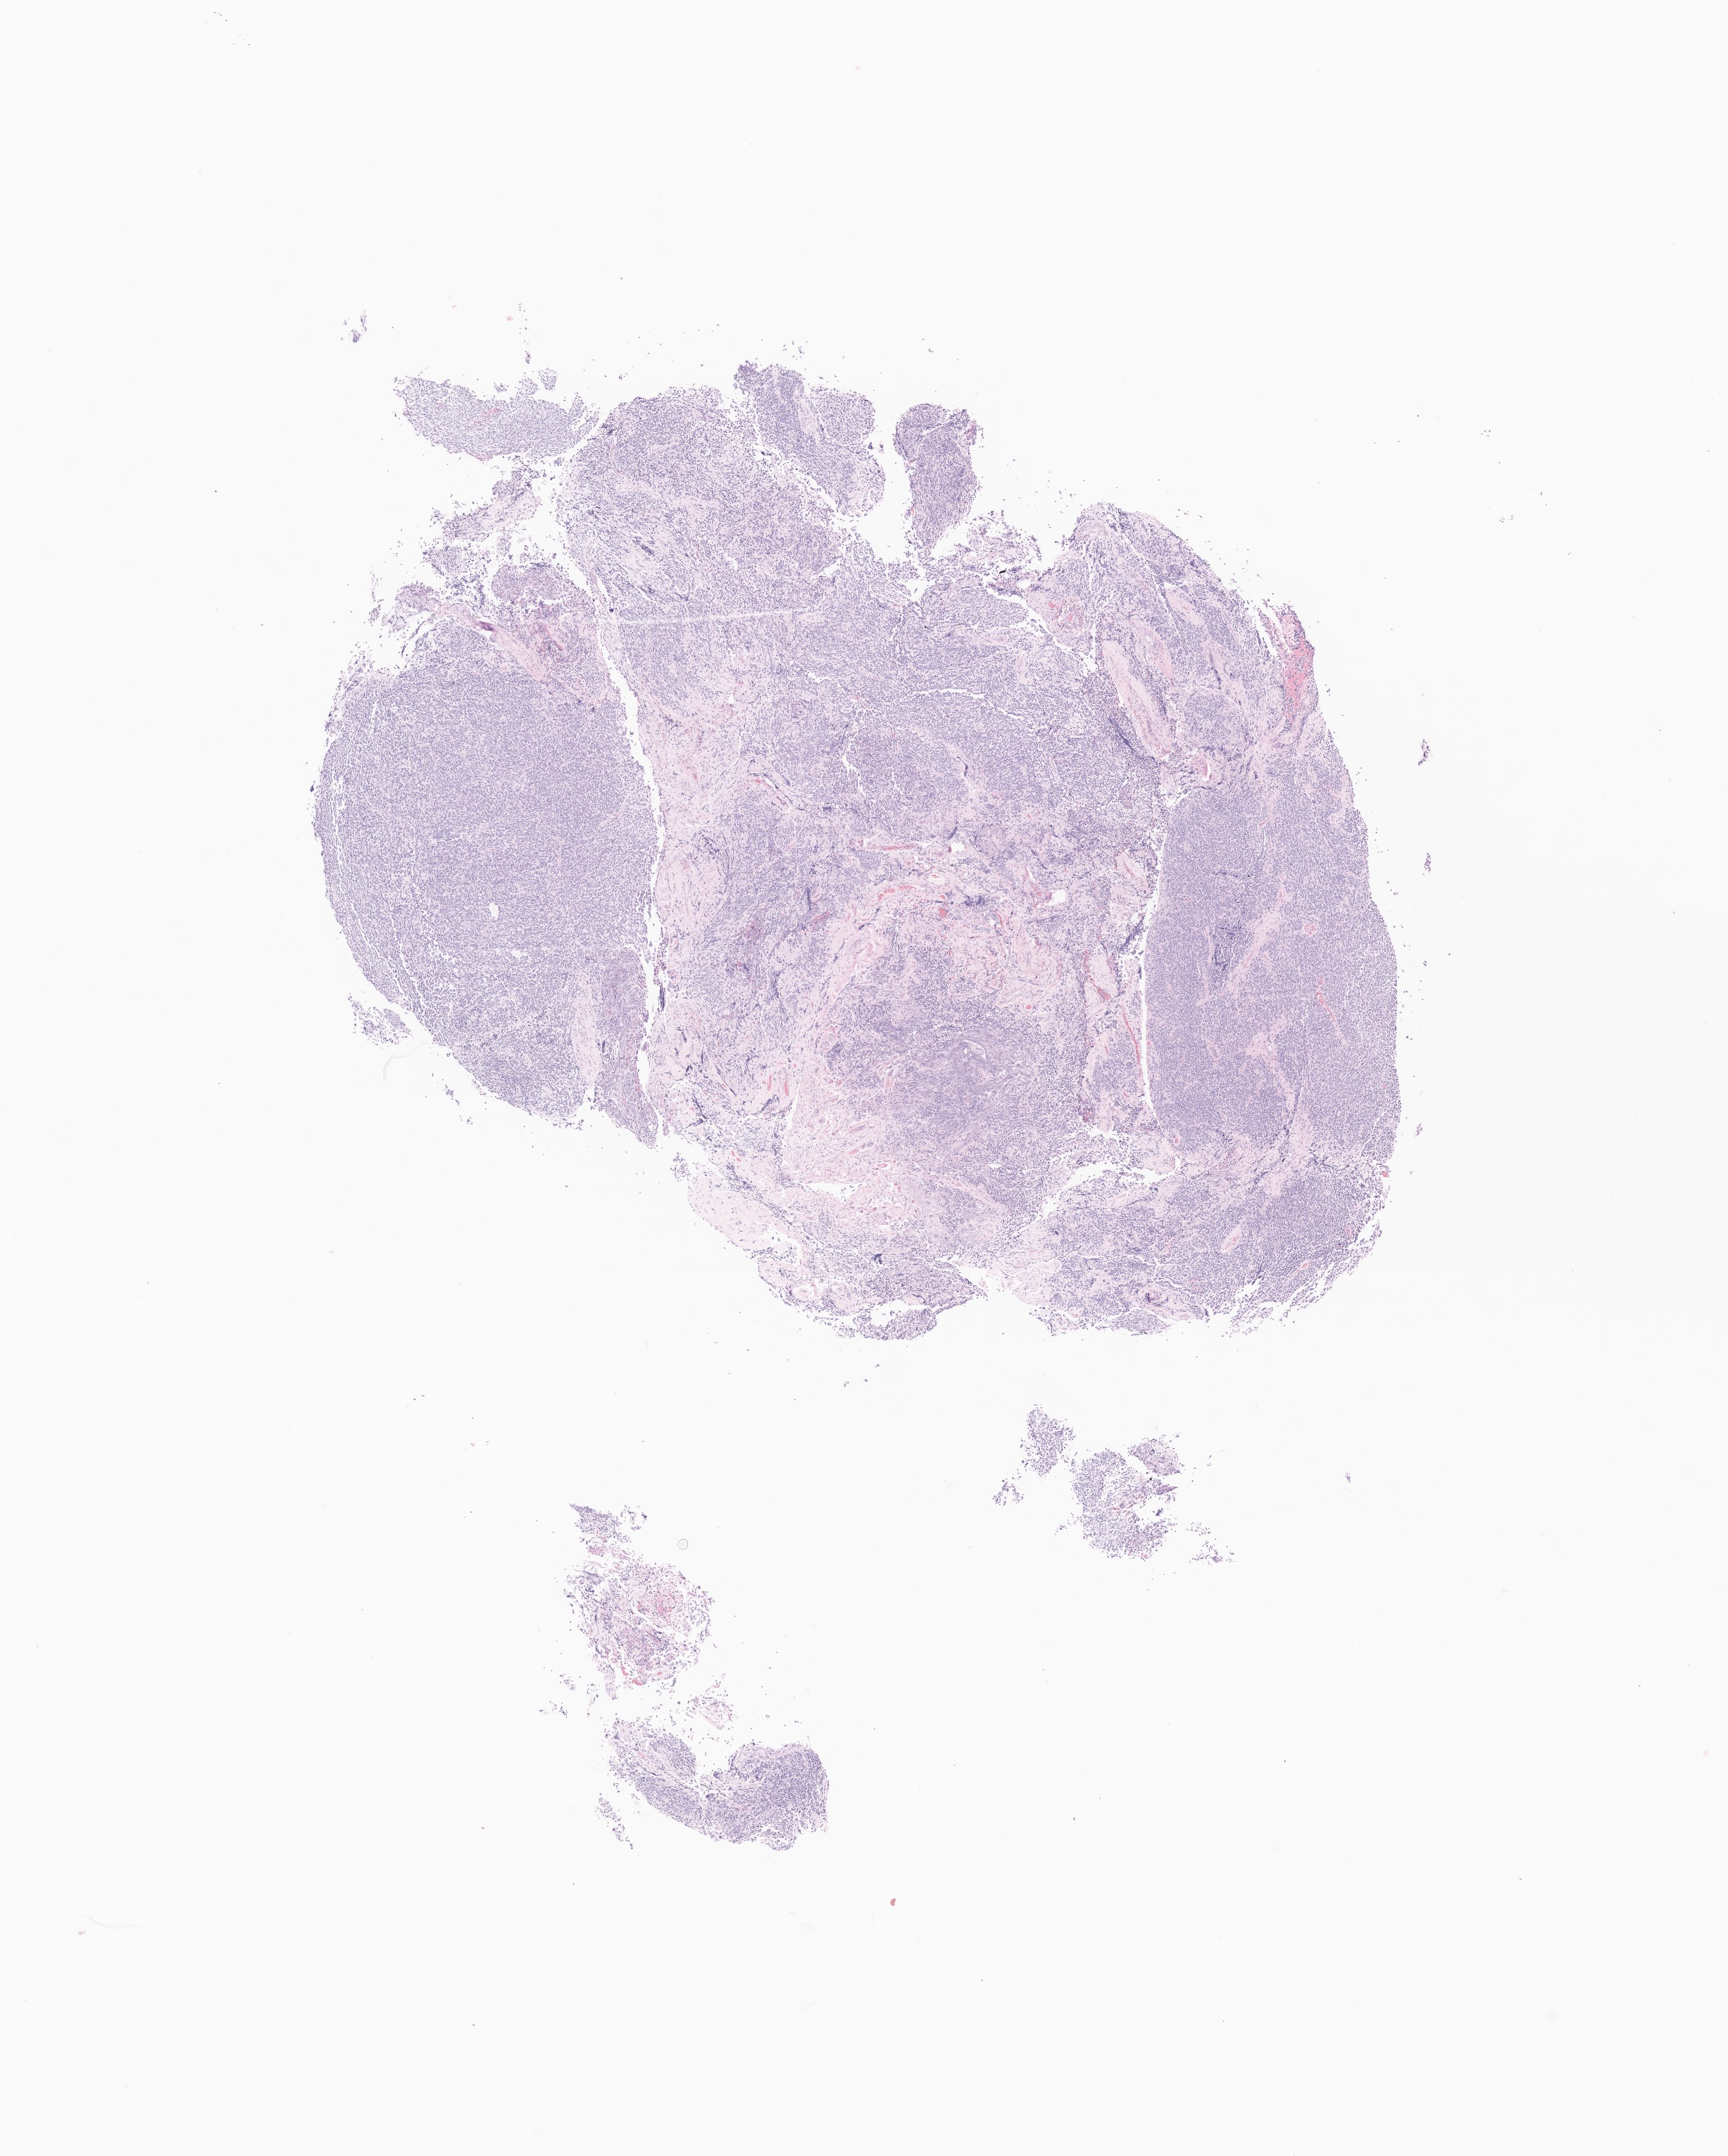
Whole-slide image, haematoxylin and eosin stain of tumor tissue from the brain — shown as a low-resolution overview of the whole scanned area (about 10.3 x 12.9 mm), FFPE section. Patient: male, age 141 months.
Diagnosis: Medulloblastoma, NOS.